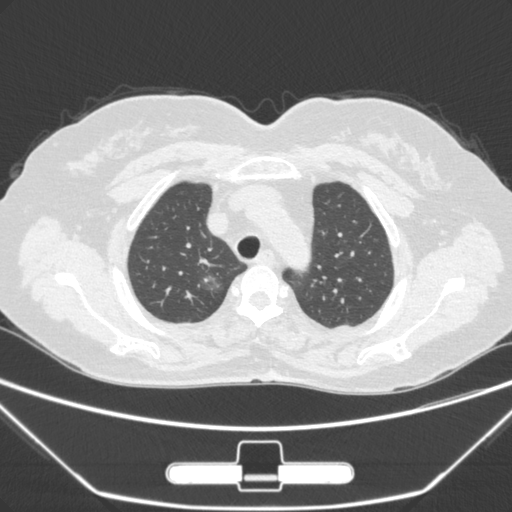
Chest CT, one axial slice; position 226 of 275 along the scan axis; lung window (W 1500 / L -600 HU); 512 × 512 image matrix, field of view 356 × 356 mm. Female patient, age 63 years. Case-level facts recorded for this patient, not image findings: clinical TNM (as recorded): T1a N0 M0; histopathological grade: G1.
Outlined on this slice (bounding box drawn by a radiologist):
- lung tumour (recorded histology: adenocarcinoma): bounding box <192,268,228,306> (left, top, right, bottom; pixels)